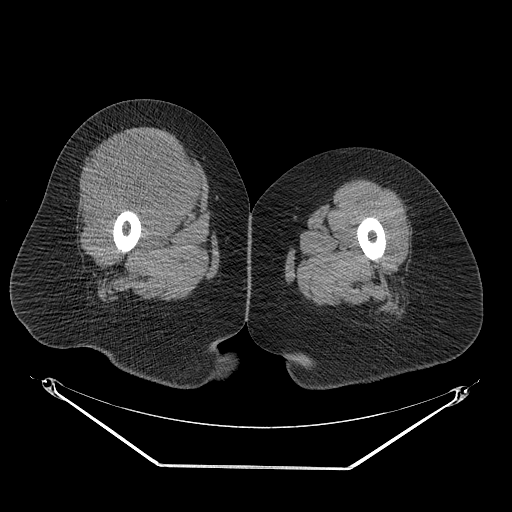
CT of an extremity soft-tissue mass (from a PET/CT study), one axial slice; position 35 of 267 along the scan axis; reconstruction kernel STANDARD; soft-tissue window (W 400 / L 40 HU); 512 × 512 image matrix, field of view 500 × 500 mm. Female patient. Case-level facts recorded for this patient, not image findings: histological type: malignant solitary fibrous tumor; grade: intermediate; site of the primary tumour: right thigh.
Annotated regions visible in this slice (expert contour drawn on MRI and transferred to this co-registered scan by the dataset authors):
- gross tumour volume including surrounding oedema: bounding box [x1, y1, x2, y2] px = [87, 132, 207, 225]
- gross tumour volume (mass): [94, 132, 204, 222]